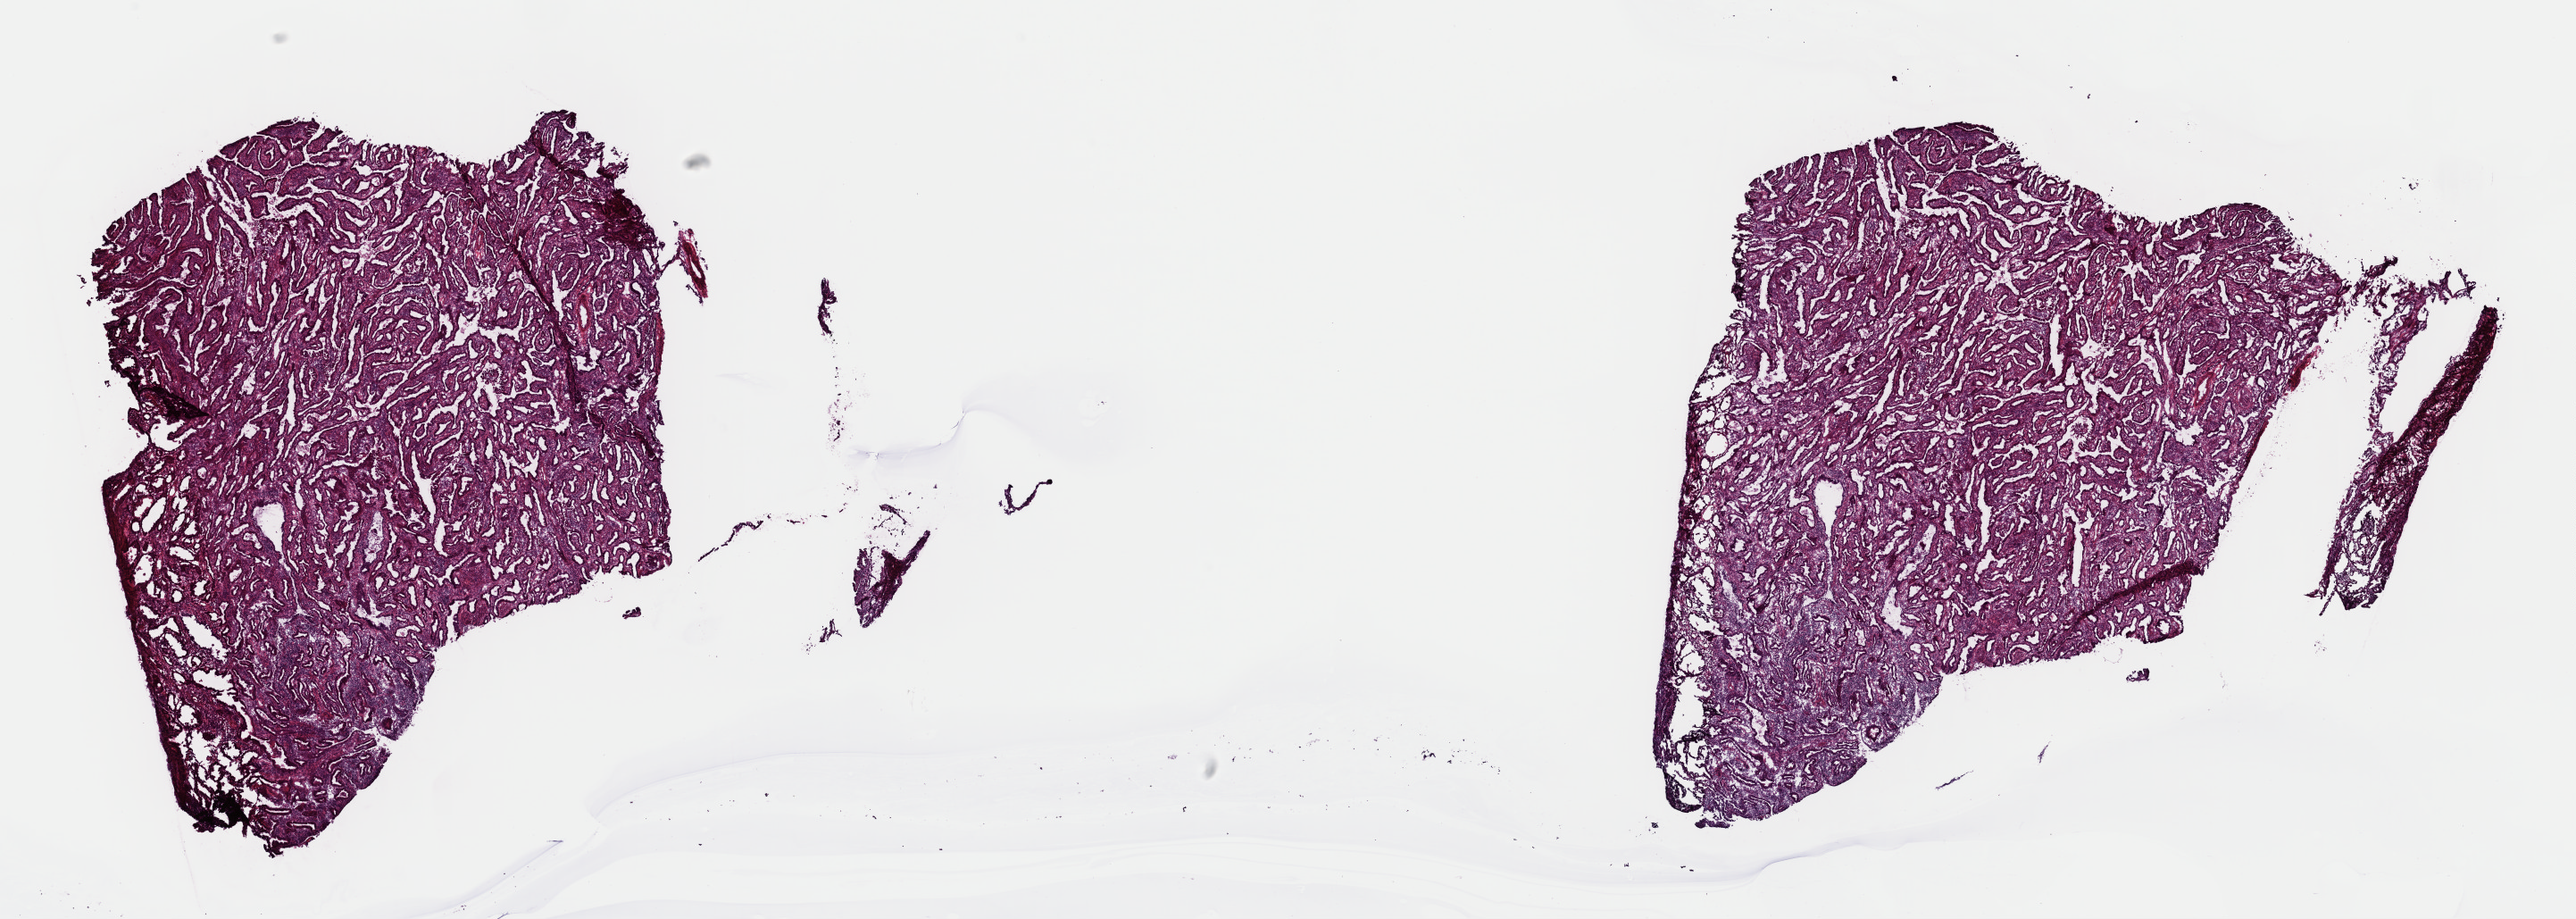
Hematoxylin and eosin (H&E) stained whole-slide image — low-resolution overview of the scanned area, about 22.8 x 8.1 mm; frozen section; cervix, primary tumour sample. Patient: female, age at initial diagnosis 38 years. Histologic grade: G1 (well differentiated). Composition of this section per pathologist review: tumour cells 80%, tumour nuclei 80%, normal cells 0%, stromal cells 10%, necrosis 10%. Infiltration values recorded for this section: lymphocyte infiltration 60%, monocyte infiltration 10%, neutrophil infiltration 20%.
Diagnosis: Adenocarcinoma, NOS (cervix uteri). Lymph nodes positive (case pathology): 0 of 20 examined. FIGO stage: IB1.